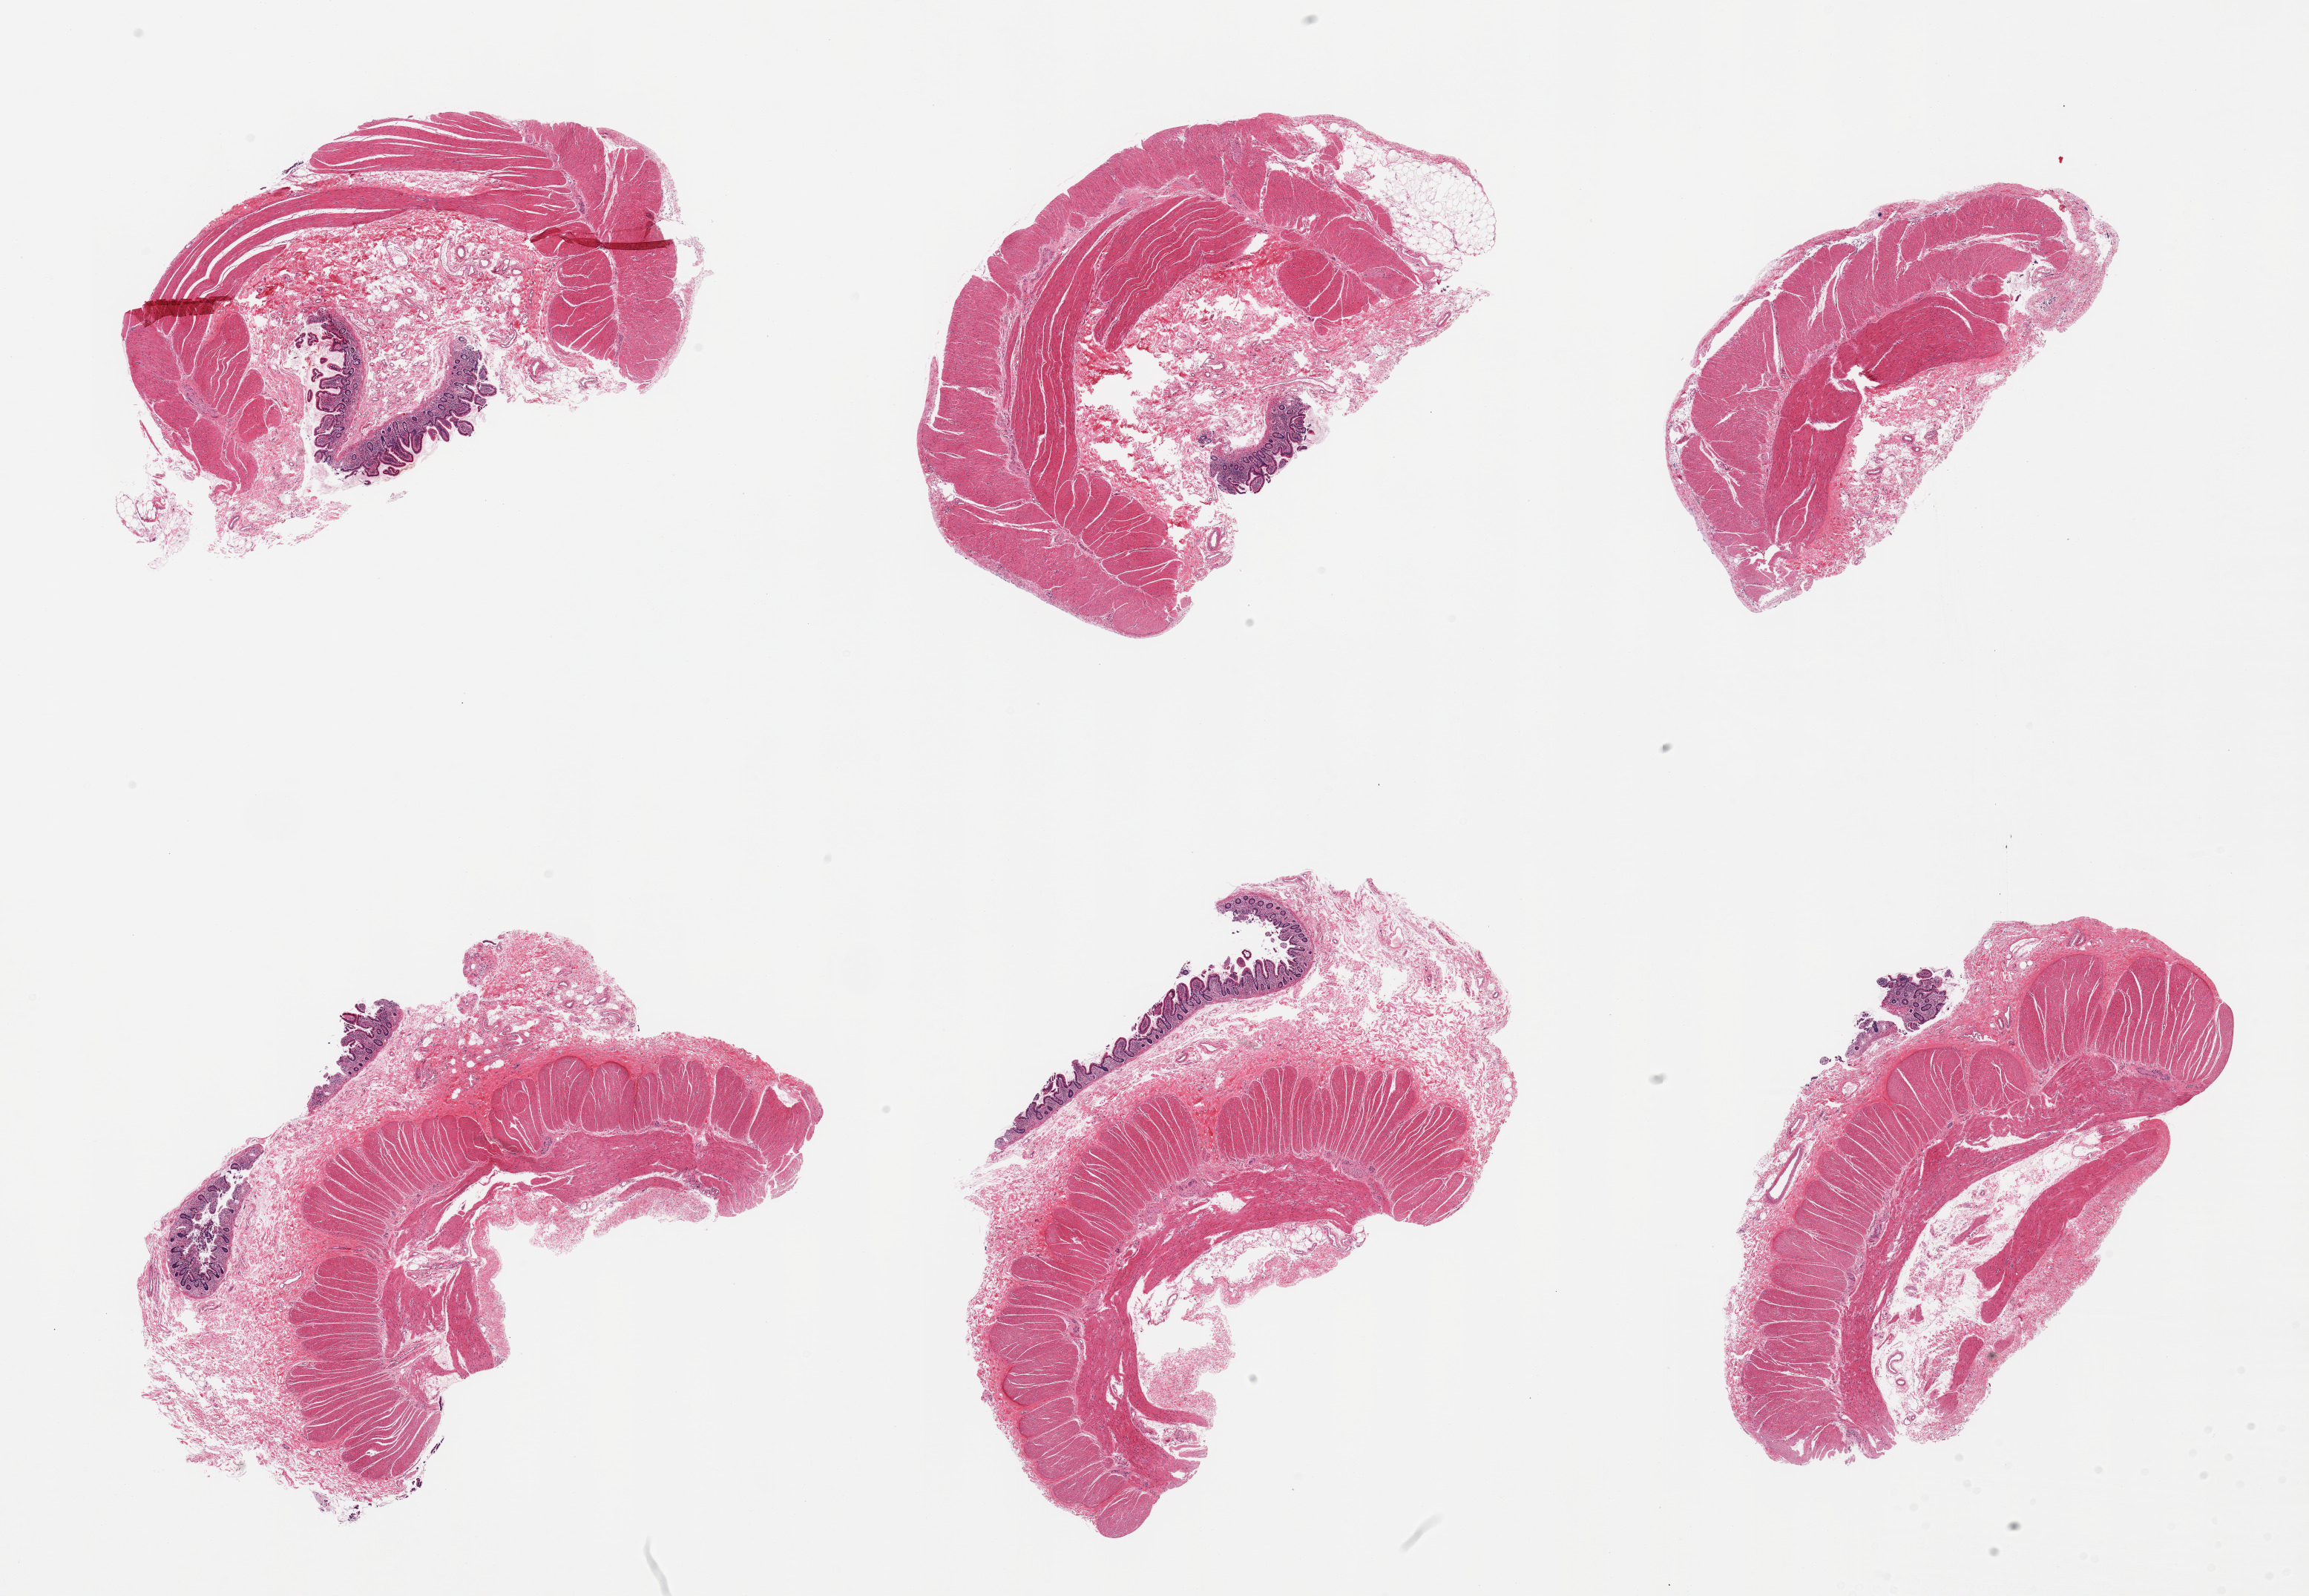
Whole-slide image, haematoxylin and eosin stain — shown as a low-resolution overview of the whole scanned area (about 24.6 x 17.0 mm, from a 20x scan); PAXgene-fixed paraffin-embedded (PFPE) section; sampled site (target tissue): ileum; donor tissue sample. Donor: male.
Pathologist's review note for this sample: 6 pieces; predominantly muscularis with incomplete strips of mucosa, no lymphoid tissue.